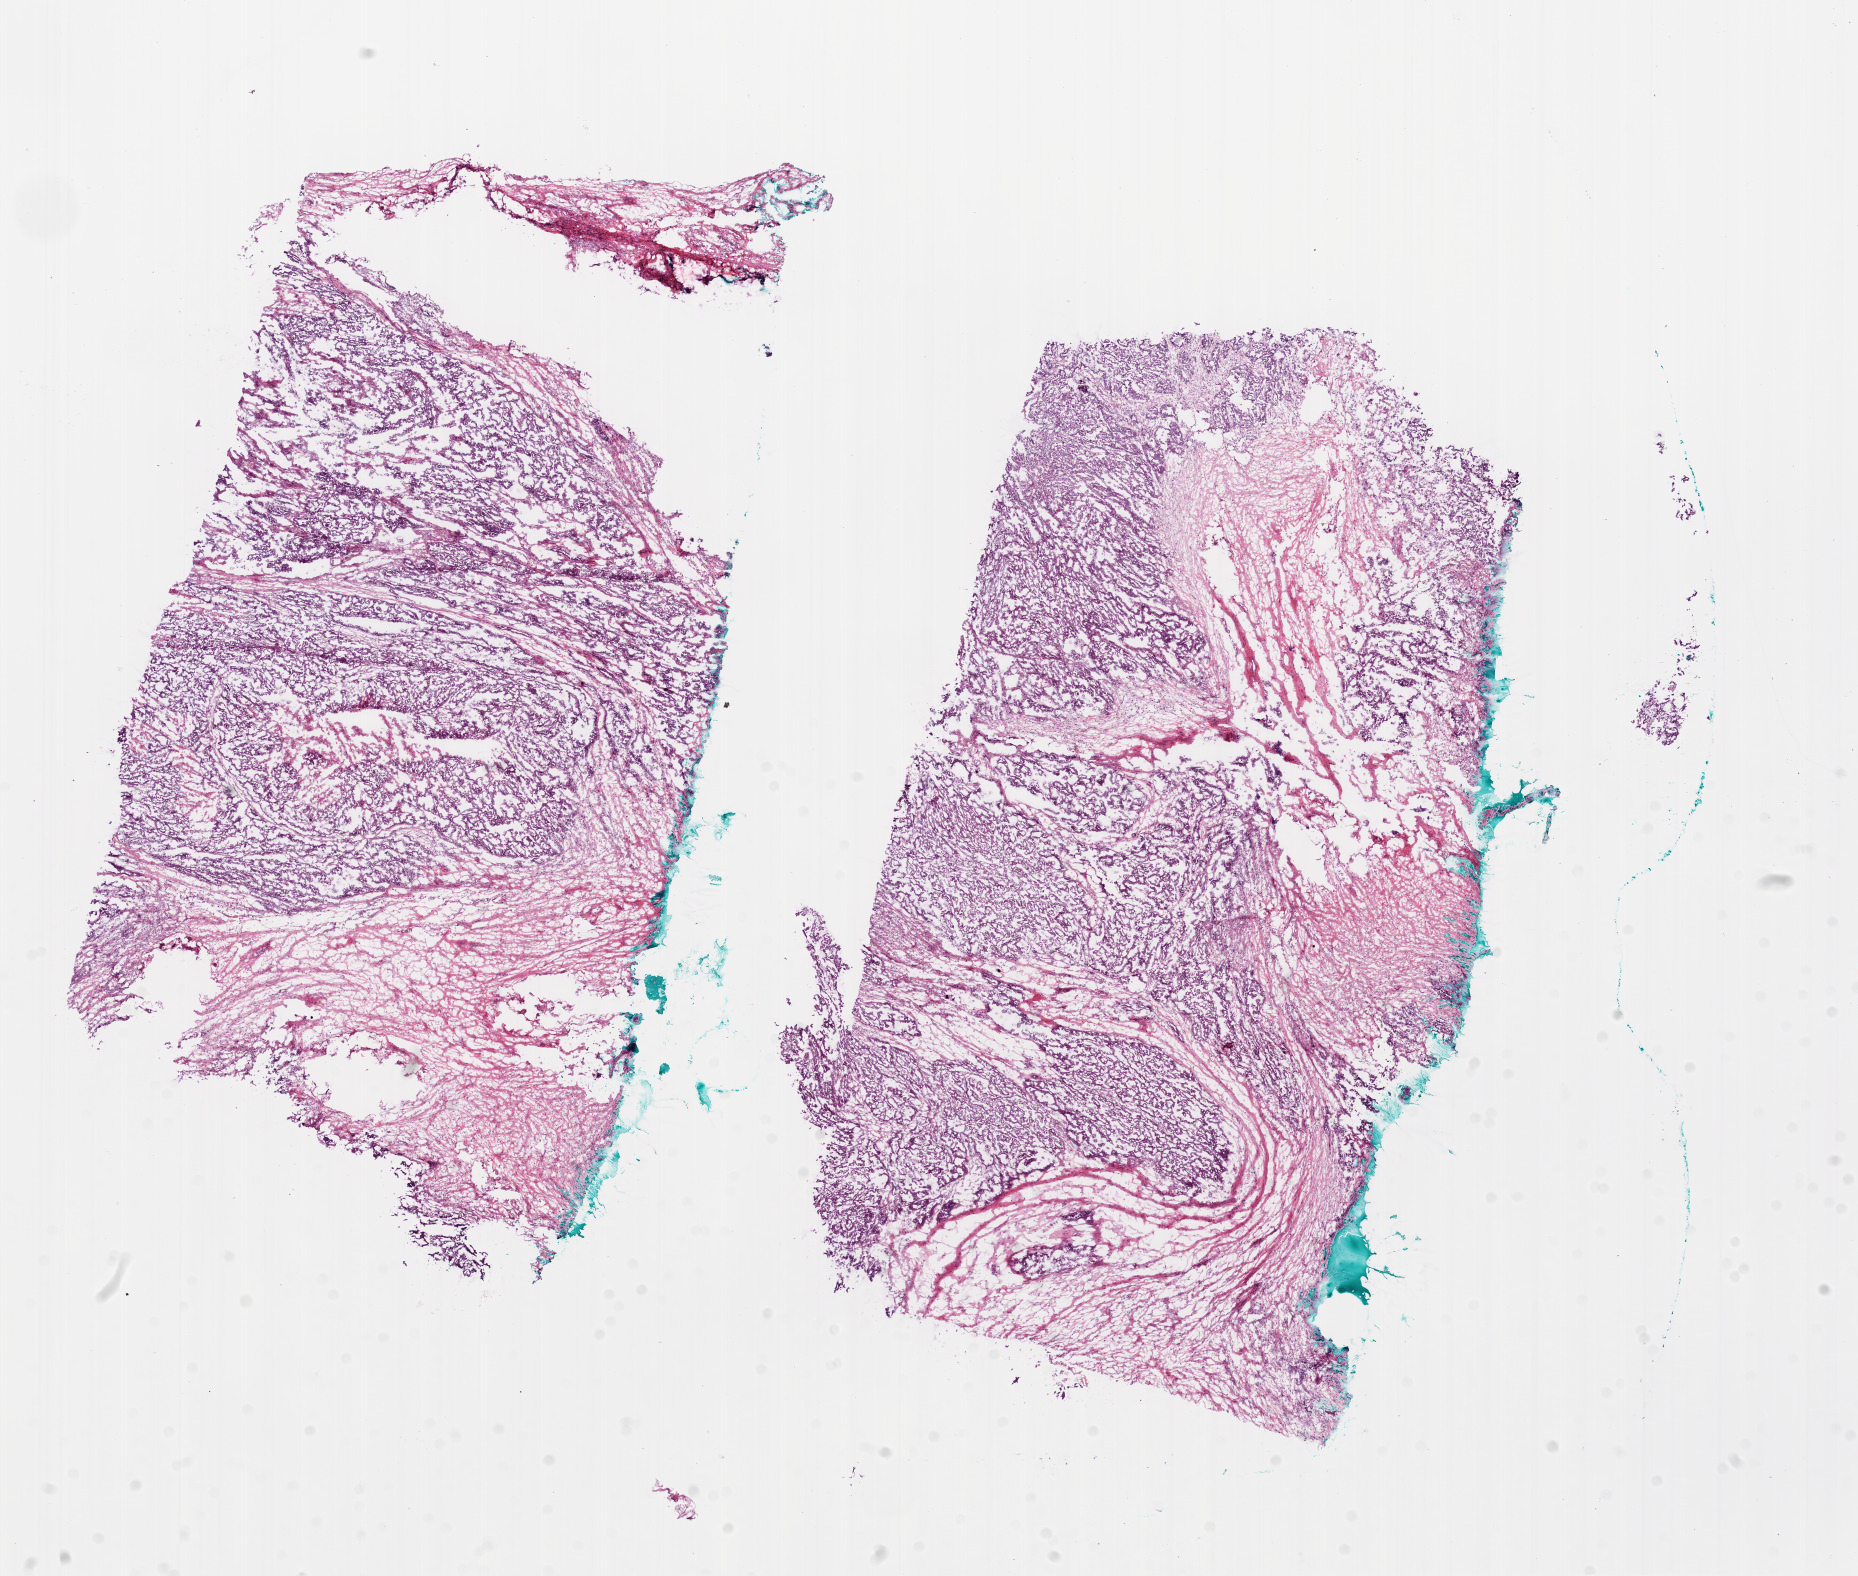
Whole-slide histology image, H&E-stained — whole scanned area (about 15.0 x 12.7 mm, acquisition: 20x scan) shown as a low-resolution overview. Frozen section from the bottom of the tissue portion. Ovary, primary tumour sample. Female, age 44 years at initial diagnosis. Histologic grade: G3 (poorly differentiated). Pathologist review of this section (percent, as recorded): tumour cells 60%, tumour nuclei 90%, normal cells 40%, necrosis 0%. Inflammatory infiltration, as recorded: lymphocyte infiltration 50%, neutrophil infiltration 50%.
Pathologic diagnosis: Serous cystadenocarcinoma, NOS. FIGO stage: IIIC.